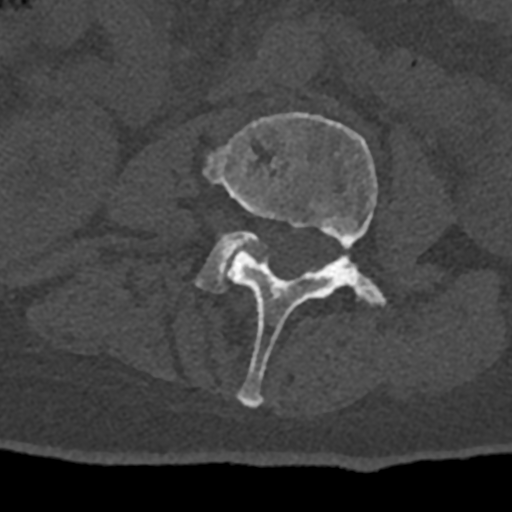
CT including the spine, one axial slice; slice 309 of 797 in the series (ordered by position); reconstruction kernel Br40s/3; 120 kVp; bone window (W 1800 / L 400 HU); 0.5 mm slice thickness; 512 × 512 image matrix. Male patient, age 74 years. From the clinical record (not read from this slice): primary cancer: renal; vertebrae with lytic lesions (as recorded): T10, L1, L2, L3, L4, L5.
Outlined on this slice (semi-automatic segmentation, software-assisted and operator-edited):
- L3 vertebra: box from (x=205, y=112) to (x=387, y=408) px
- L4 vertebra: (x=197, y=231)–(x=266, y=292)